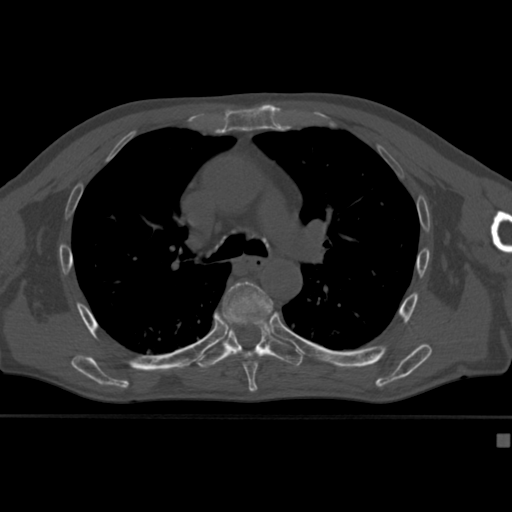
CT including the spine, one axial slice; reconstruction kernel Br40s; bone window (W 1800 / L 400 HU); 1.5 mm slice thickness; 512 × 512 image matrix. Male patient, age 64 years. Case-level facts recorded for this patient, not image findings: primary cancer: uterus; vertebrae with lytic lesions (as recorded): T1, T4, T5, T7, L5.
Outlined on this slice (semi-automatic segmentation, software-assisted and operator-edited):
- T6 vertebra: box from (x=202, y=280) to (x=274, y=382) px
- T7 vertebra: (x=197, y=317)–(x=304, y=372)